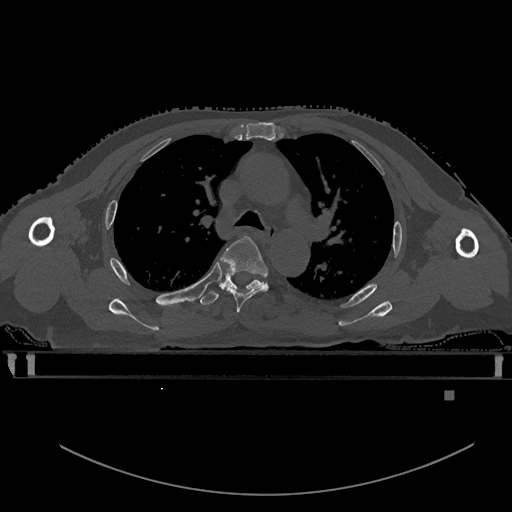
CT including the spine, one axial slice. Slice 387 of 969 in the series (ordered by position). Bone window (W 1800 / L 400 HU). 0.5 mm slice thickness. 512 × 512 image matrix, field of view 456 × 456 mm. Male patient, age 82 years. From the clinical record (not read from this slice): primary cancer: prostate; vertebrae with lytic lesions (as recorded): T11, T9, T8, T2.
Outlined on this slice (semi-automatic segmentation, software-assisted and operator-edited):
- T4 vertebra: bounding box (x1, y1, x2, y2) in pixels: (220, 235, 268, 313)
- T5 vertebra: (200, 272, 263, 306)